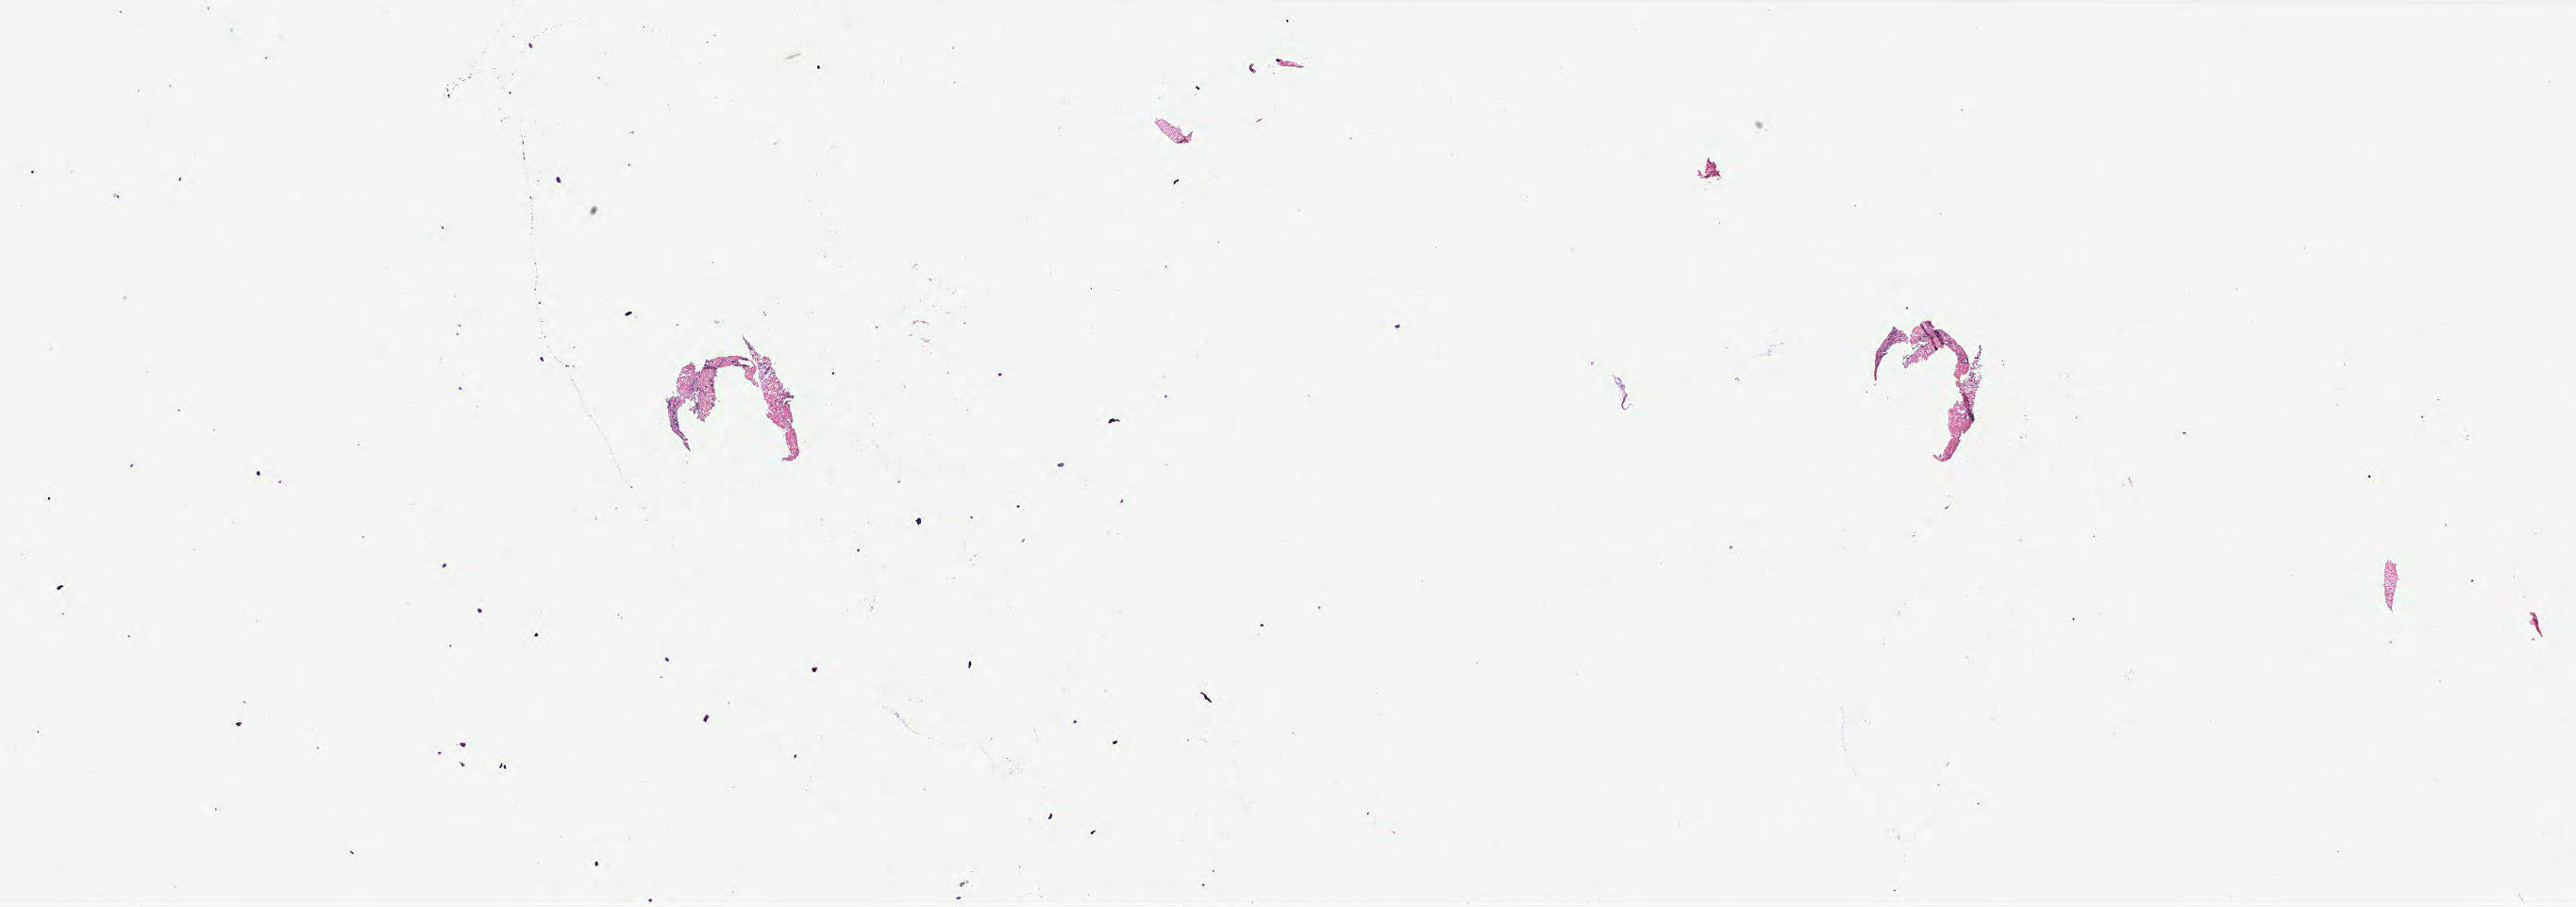
Digitized Hematoxylin and eosin (H&E) stained tissue section (whole slide), a low-resolution overview of the entire scanned area, about 43.7 x 15.4 mm (from a 40x scan); breast, tissue type not recorded.
Patient diagnosis (cohort enrolment): breast cancer (breast).